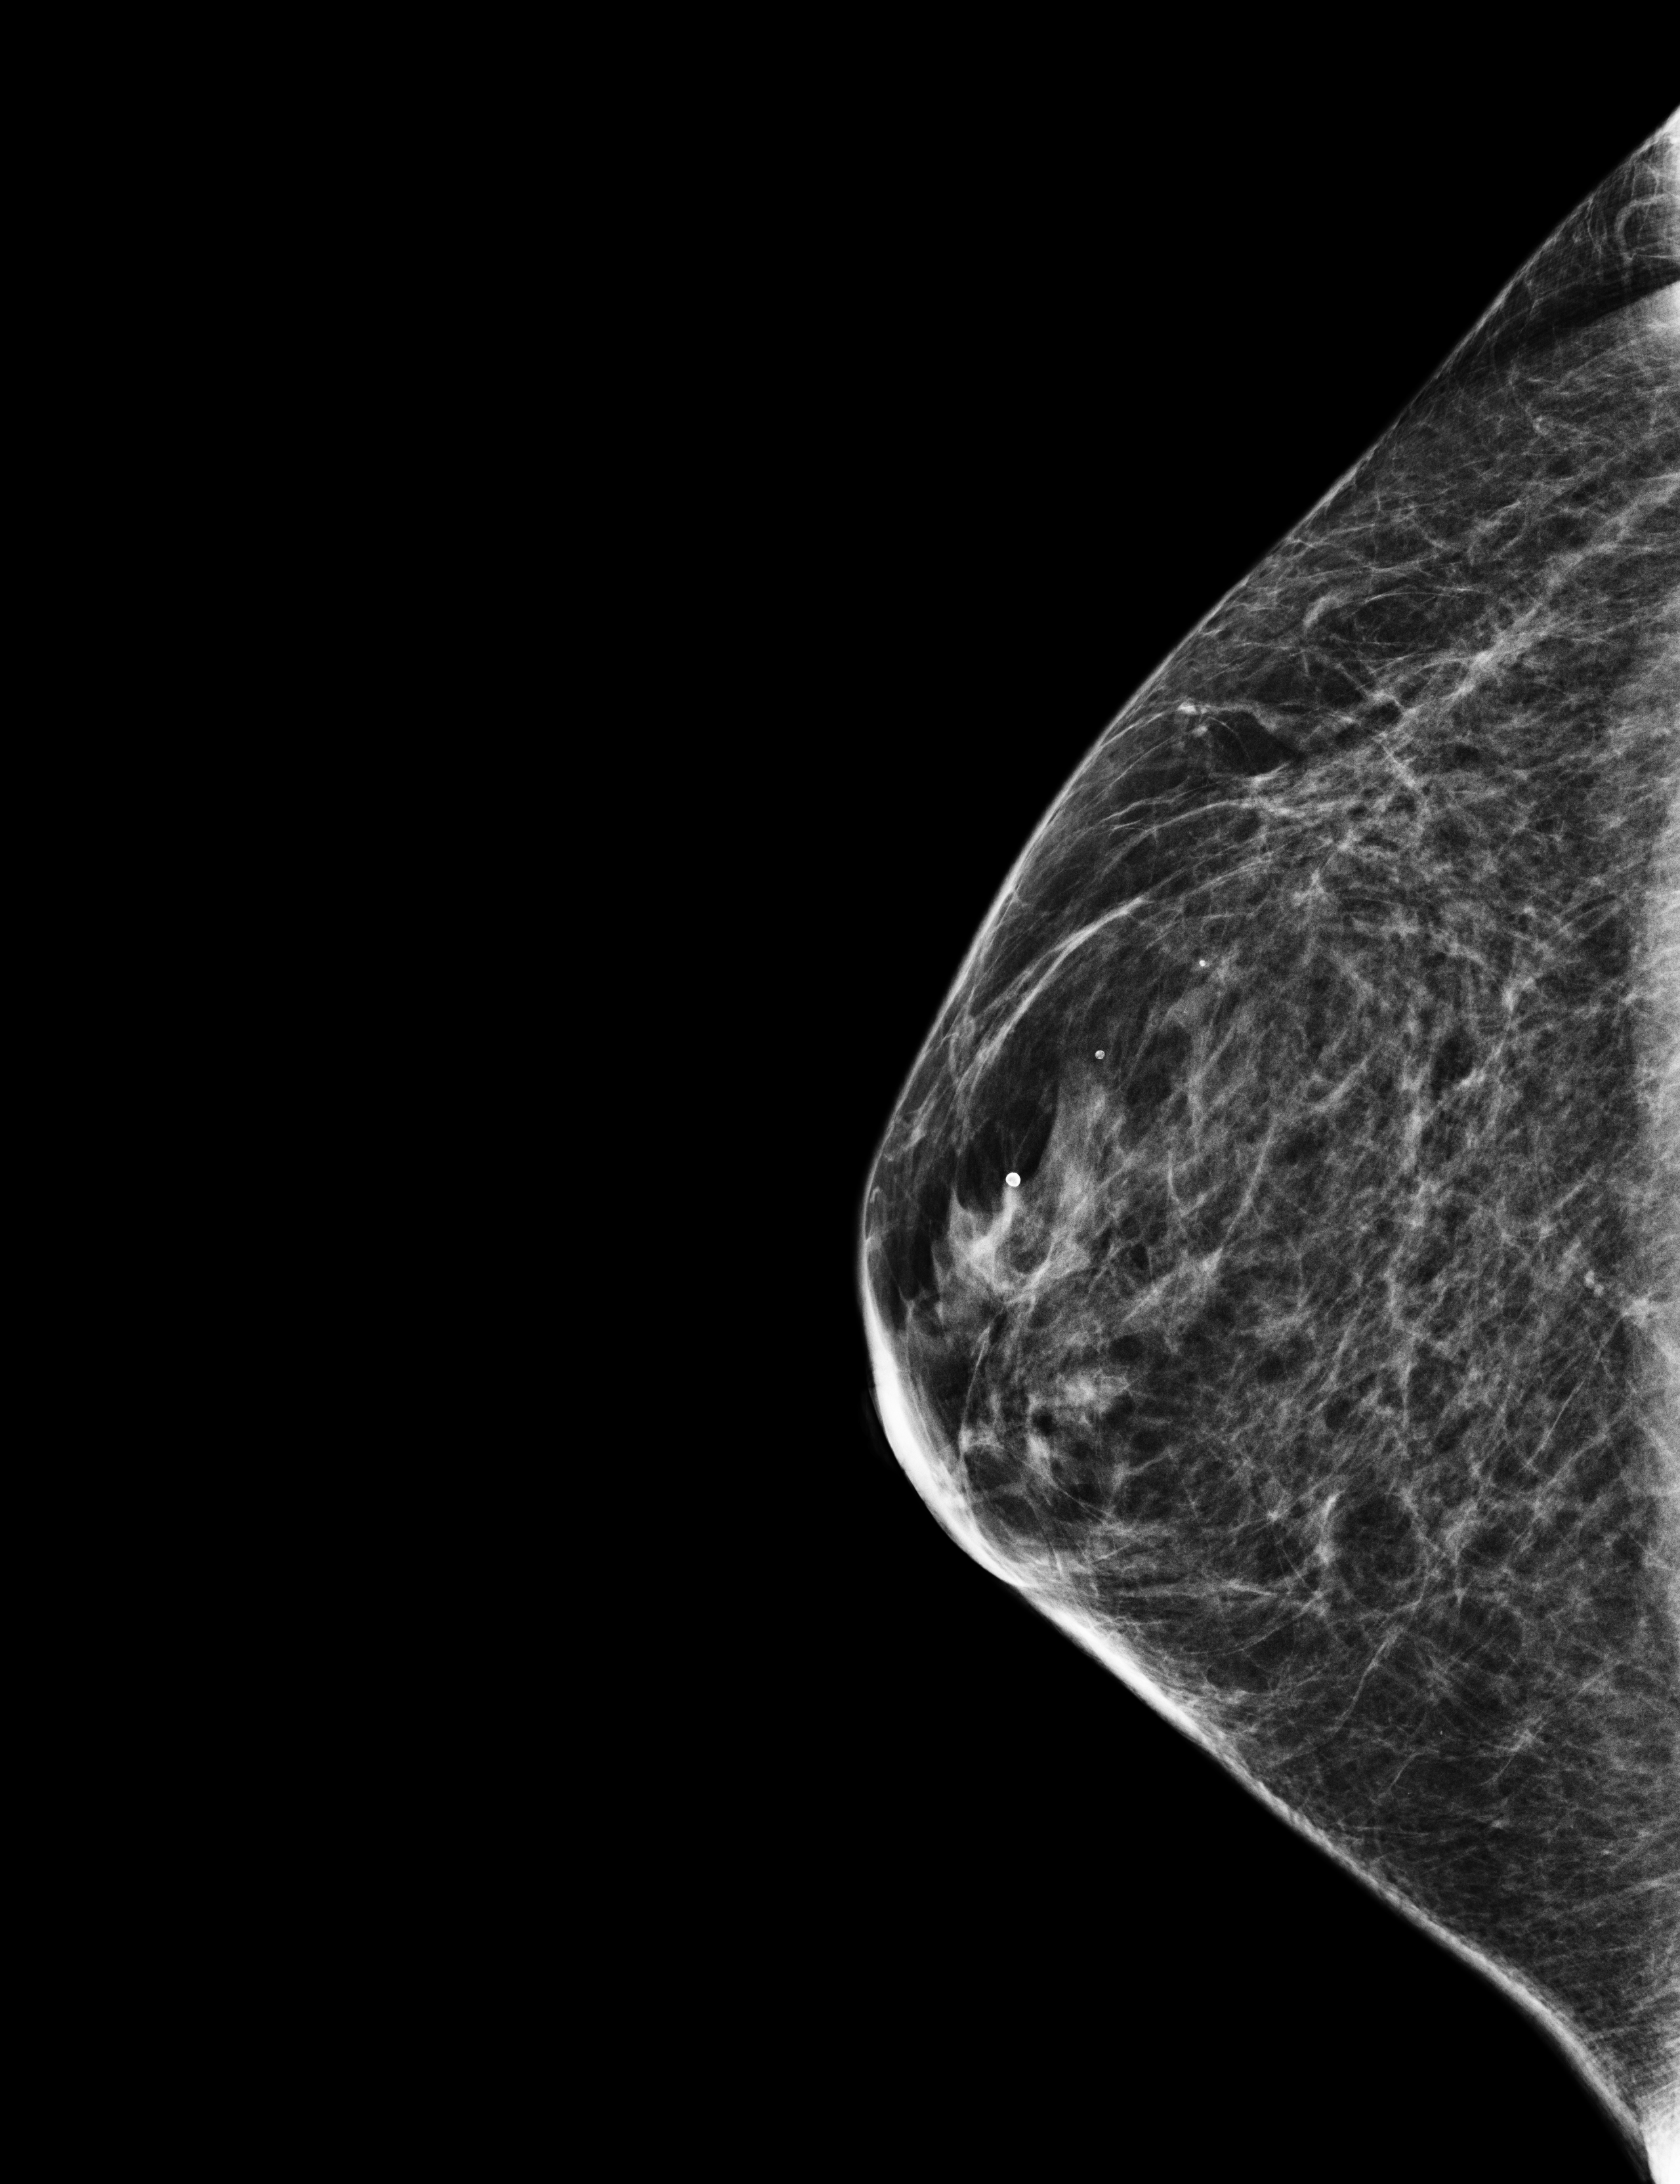
Screening examination, system: Selenia Dimensions. Patient aged 51 years (female).
Image type: full-field digital mammogram. Breast: right. Projection: CC view. Breast density at the screening exam (both breasts): heterogeneously dense (BI-RADS density category c). Final BI-RADS assessment for this screening round (tomosynthesis exam, both breasts): category 2. Recall: no recall after this screen.